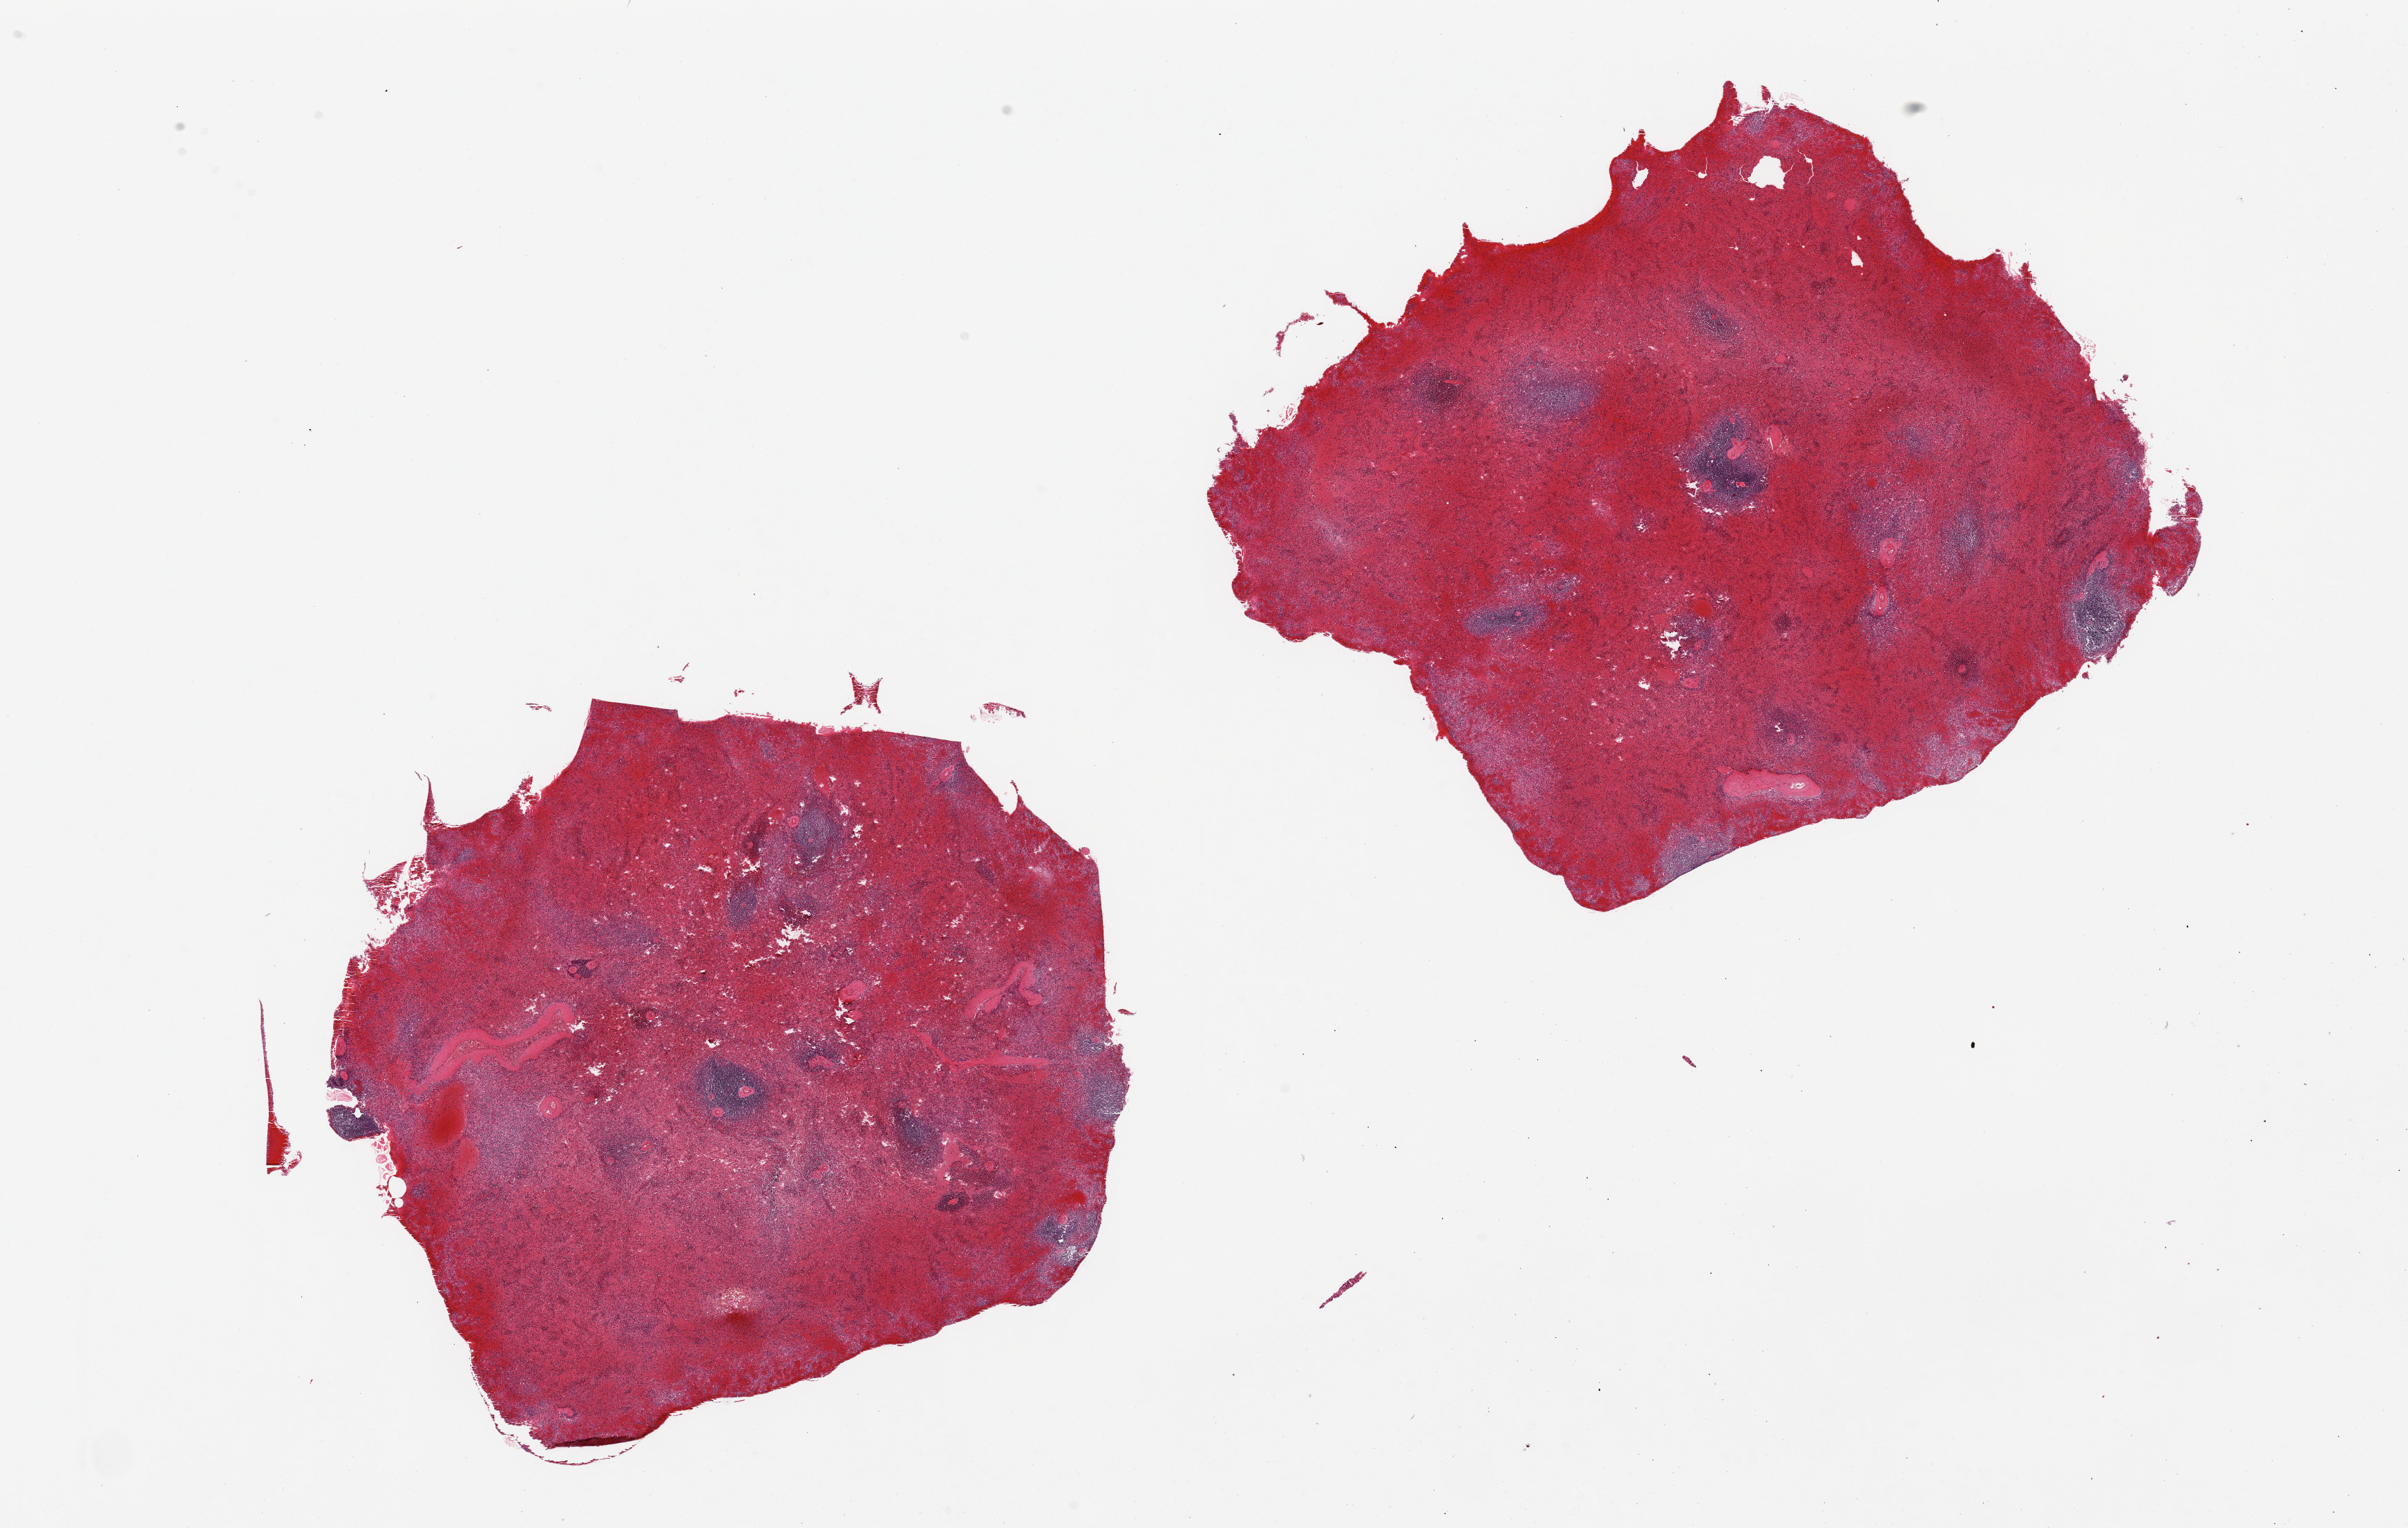
Digitized H&E-stained section, shown as a low-resolution overview of the whole scanned area (about 27.6 x 17.5 mm). PAXgene-fixed, paraffin-embedded tissue. Sampled site (target tissue): spleen. Tissue donor sample. Donor sex: male.
Pathologist's review note for this sample: 2 pieces; severe congestion.